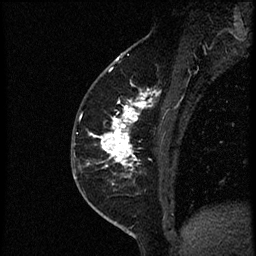
Breast MRI (dynamic contrast-enhanced), one sagittal slice. Slice 27 of 56 in the series (ordered by position). Dynamic contrast-enhanced study with each time point stored as its own series, time point 2 of 4 at this slice position (early post-contrast, ordered by acquisition time). 1.5 T. TE 4.2 ms, TR 18.9 ms. 2 mm slice thickness. 256 × 256 image matrix, field of view 200 × 200 mm. Female patient. Case-level facts recorded for this patient, not image findings: setting: breast cancer imaged before/during neoadjuvant chemotherapy; receptor status: HER2-positive.
Outlined on this slice (semi-automatically segmented with operator editing):
- analysis volume of interest (the breast-tissue region the enhancement analysis was run in; not a lesion): bounding box (x1, y1, x2, y2) in pixels: (82, 85, 174, 189)
- tumour enhancement mask (voxels above the 100 % enhancement threshold inside the analysis volume of interest): (91, 89, 153, 176)